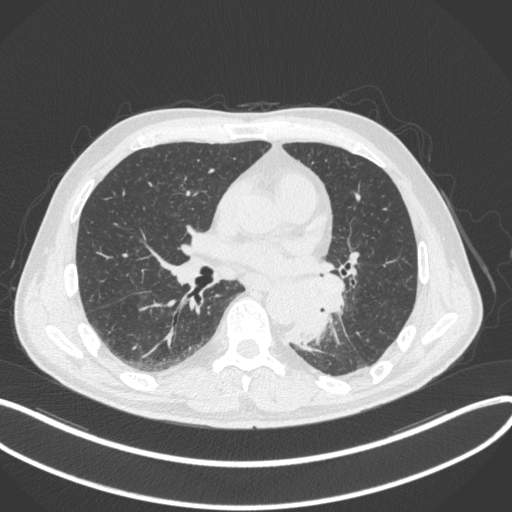
Chest CT, one axial slice; slice 165 of 328 in the series (ordered by position); reconstruction kernel B31f; 120 kVp; lung window (W 1500 / L -600 HU); 1 mm slice thickness; 512 × 512 image matrix, field of view 400 × 400 mm. Patient: male, 59 years. Case-level facts recorded for this patient, not image findings: clinical TNM (as recorded): T2a N2 M0.
Outlined on this slice (bounding box drawn by a radiologist):
- lung tumour (recorded histology: squamous cell carcinoma): box from (x=292, y=276) to (x=351, y=345) px